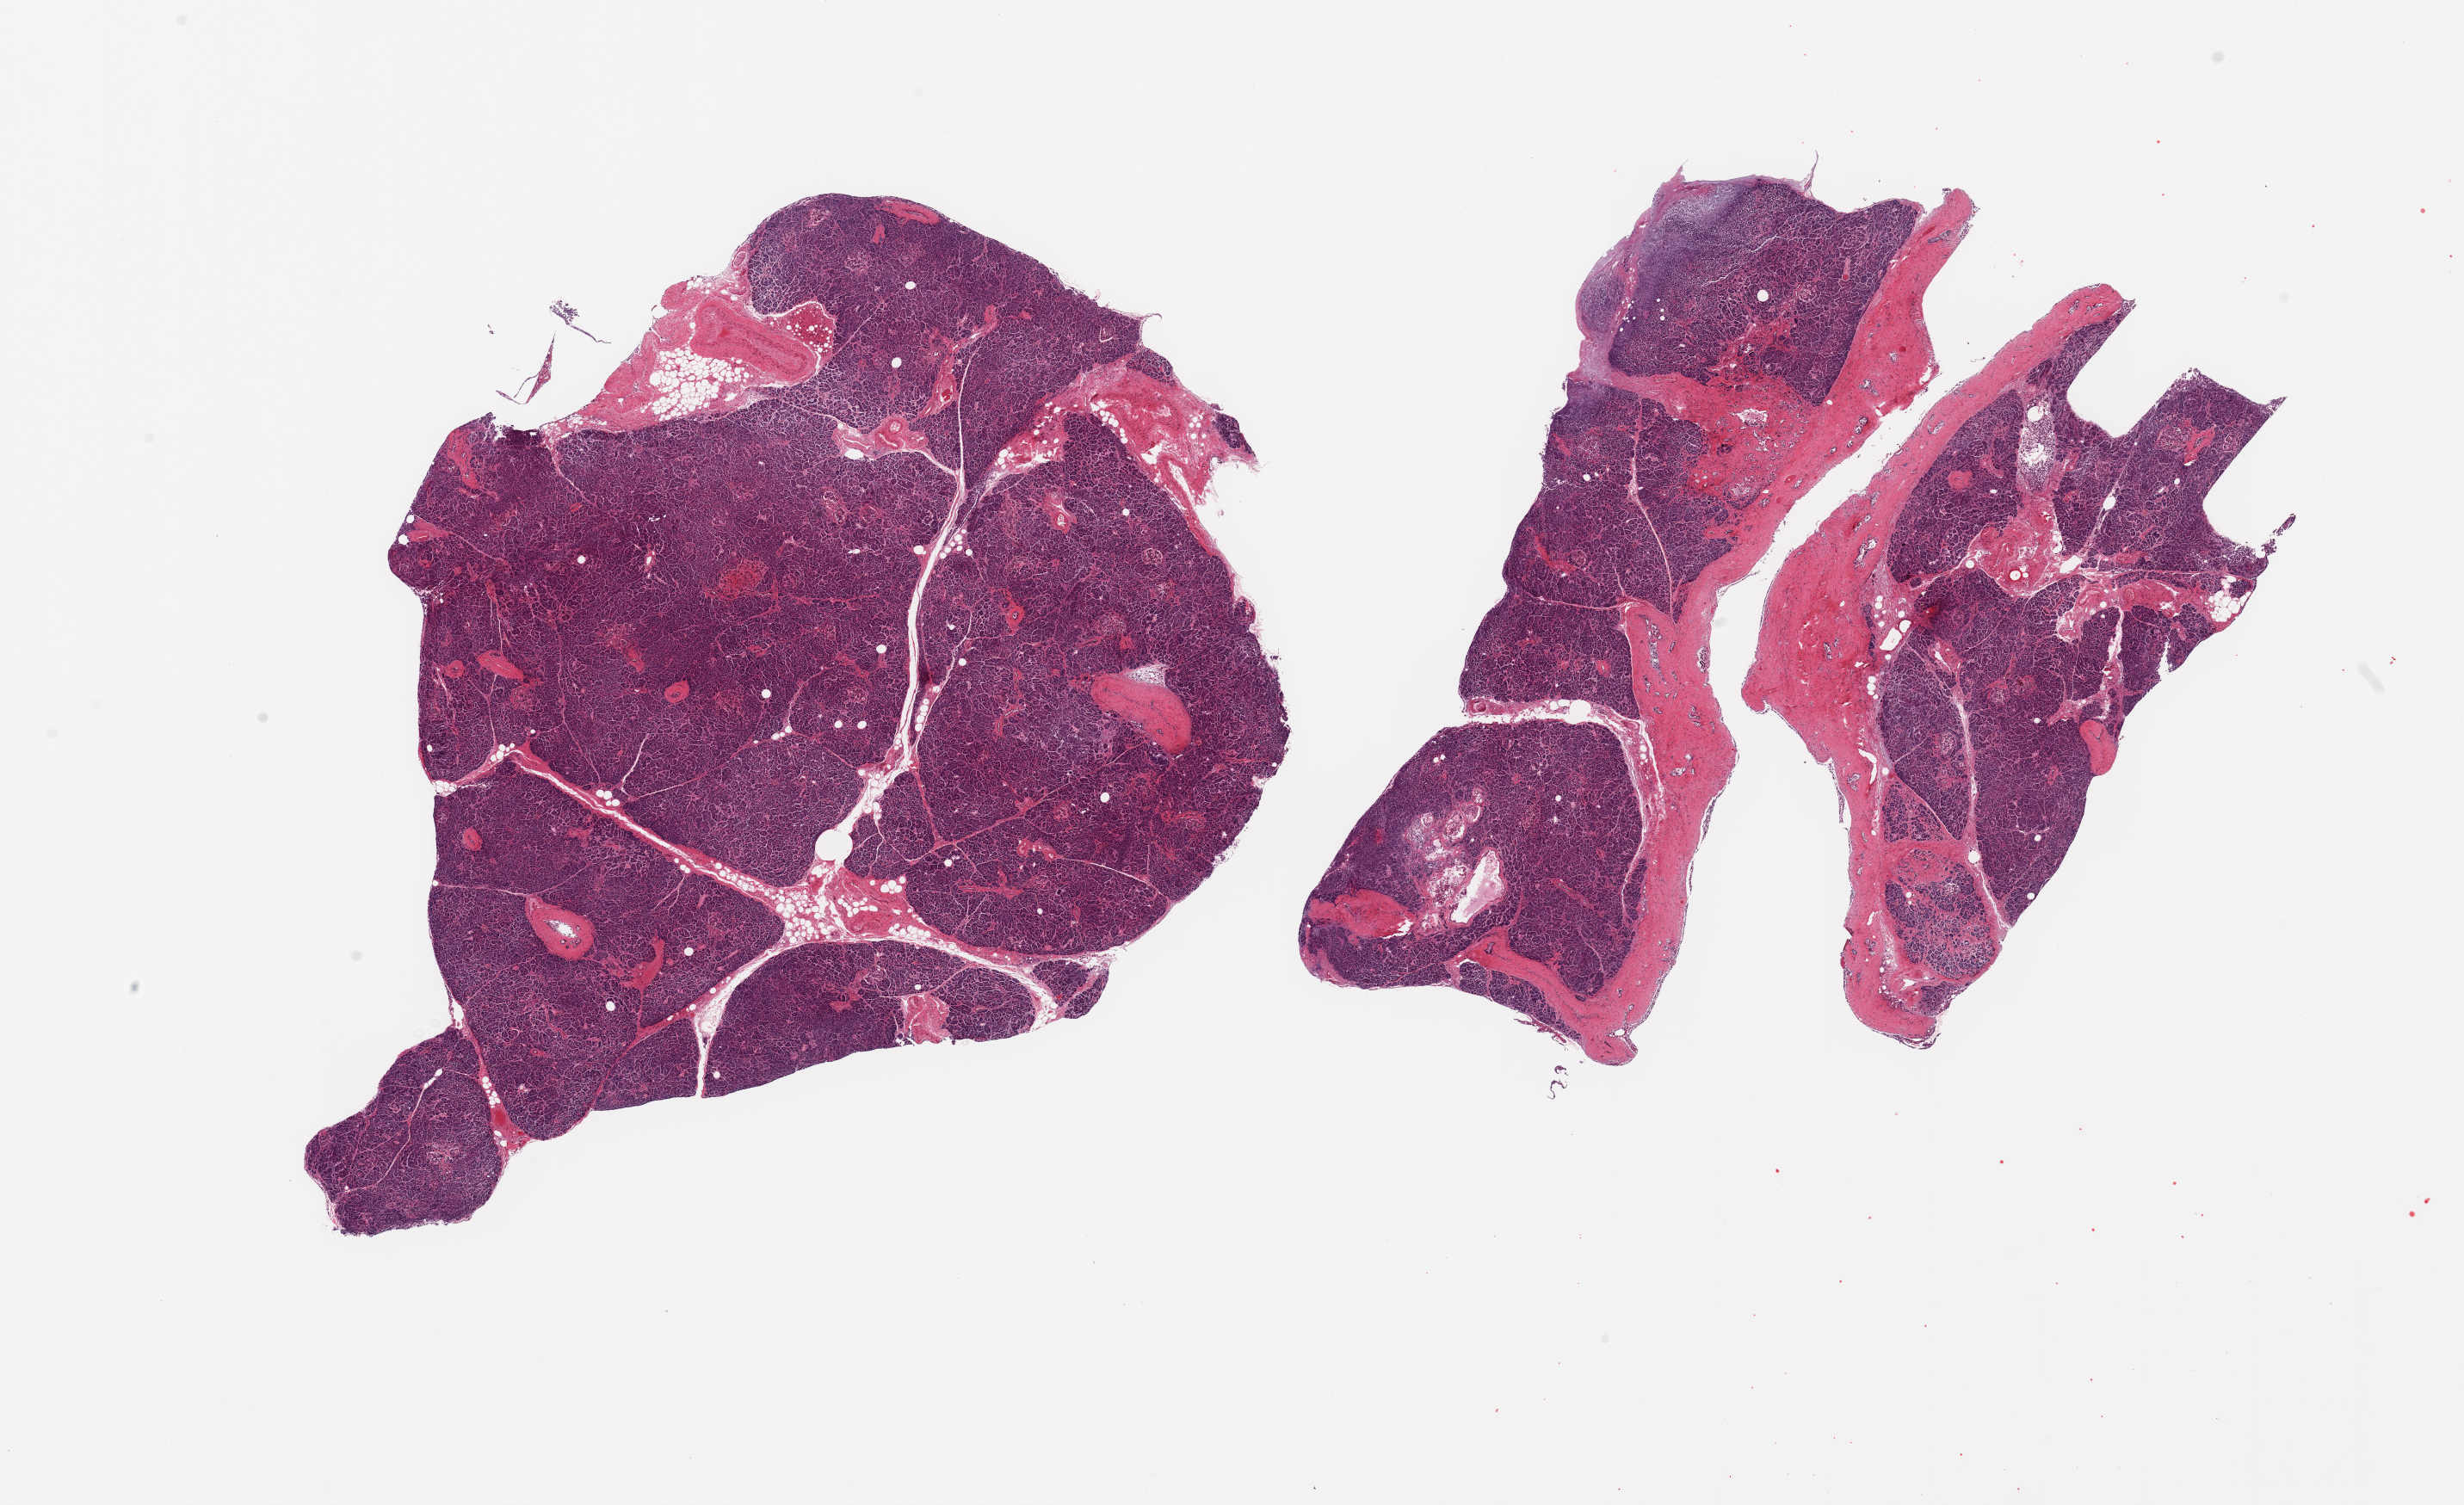
Haematoxylin and eosin whole-slide image, brightfield — a low-resolution overview of the entire scanned area, about 22.6 x 13.8 mm (acquisition: 20x scan), PAXgene-fixed, paraffin-embedded tissue, sampled site (target tissue): pancreas, tissue donor sample. Donor sex: female.
Pathologist's review note for this sample: 2 pieces, moderately advanced saponification; Islets still visible but degrading.